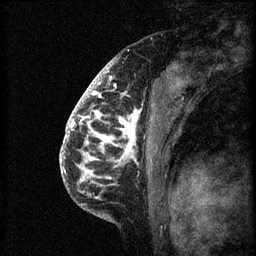
Breast MRI (dynamic contrast-enhanced), one sagittal slice; 3 images stored at this slice position (order not interpretable as contrast timing); 1.5 T; TE 4.2 ms, TR 8.2 ms; 2 mm slice thickness; 256 × 256 image matrix, field of view 180 × 180 mm. Female patient, age 41 years.
Annotated regions visible in this slice (semi-automatically segmented with operator editing):
- analysis volume of interest (the breast-tissue region the enhancement analysis was run in; not a lesion): bounding box [x1, y1, x2, y2] px = [72, 108, 159, 205]
- tumour enhancement mask (voxels above the 70 % enhancement threshold inside the analysis volume of interest): [72, 108, 140, 179]